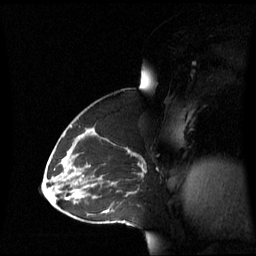
Breast MRI (dynamic contrast-enhanced), one sagittal slice; position 36 of 60 along the scan axis; dynamic contrast-enhanced series, image 2 of 3 at this slice position (ordered by acquisition); 1.5 T; TE 4.2 ms, TR 8.4 ms; 2.8 mm slice thickness; 256 × 256 image matrix, field of view 270 × 270 mm. Female patient, age 43 years. Case-level facts recorded for this patient, not image findings: setting: breast cancer imaged before/during neoadjuvant chemotherapy; receptor status: triple-negative.
Outlined on this slice (semi-automatically segmented with operator editing):
- analysis volume of interest (the breast-tissue region the enhancement analysis was run in; not a lesion): bounding box <69,137,143,198> (left, top, right, bottom; pixels)
- tumour enhancement mask (voxels above the 70 % enhancement threshold inside the analysis volume of interest): <126,148,143,196>